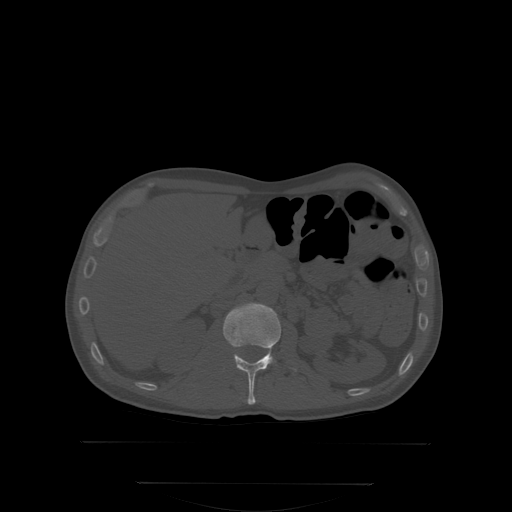
CT including the spine, one axial slice; slice 151 of 350 in the series (ordered by position); bone window (W 1800 / L 400 HU); 2.5 mm slice thickness; 512 × 512 image matrix. Male patient, age 58 years. Case-level facts recorded for this patient, not image findings: primary cancer: prostate.
Outlined on this slice (semi-automatic segmentation, software-assisted and operator-edited):
- L1 vertebra: bounding box <224,304,297,404> (left, top, right, bottom; pixels)